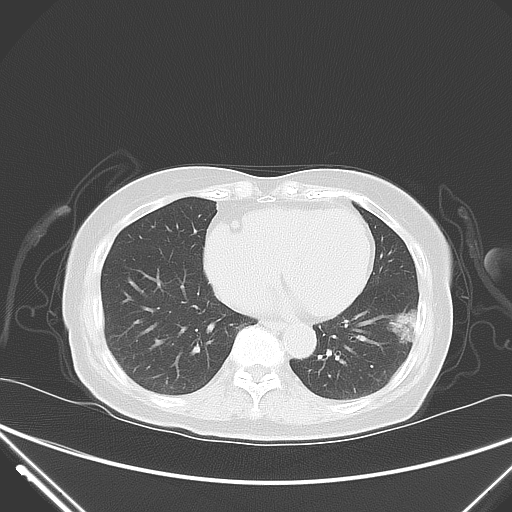
Chest CT, one axial slice. Slice 22 of 62 in the series (ordered by position). Lung window (W 1500 / L -600 HU). 5 mm slice thickness. 512 × 512 image matrix, field of view 377 × 377 mm. Patient: female, 82 years. Case-level facts recorded for this patient, not image findings: clinical TNM (as recorded): T1c N0 M0.
Outlined on this slice (bounding box drawn by a radiologist):
- lung tumour (recorded histology: adenocarcinoma): box from (x=384, y=300) to (x=426, y=353) px